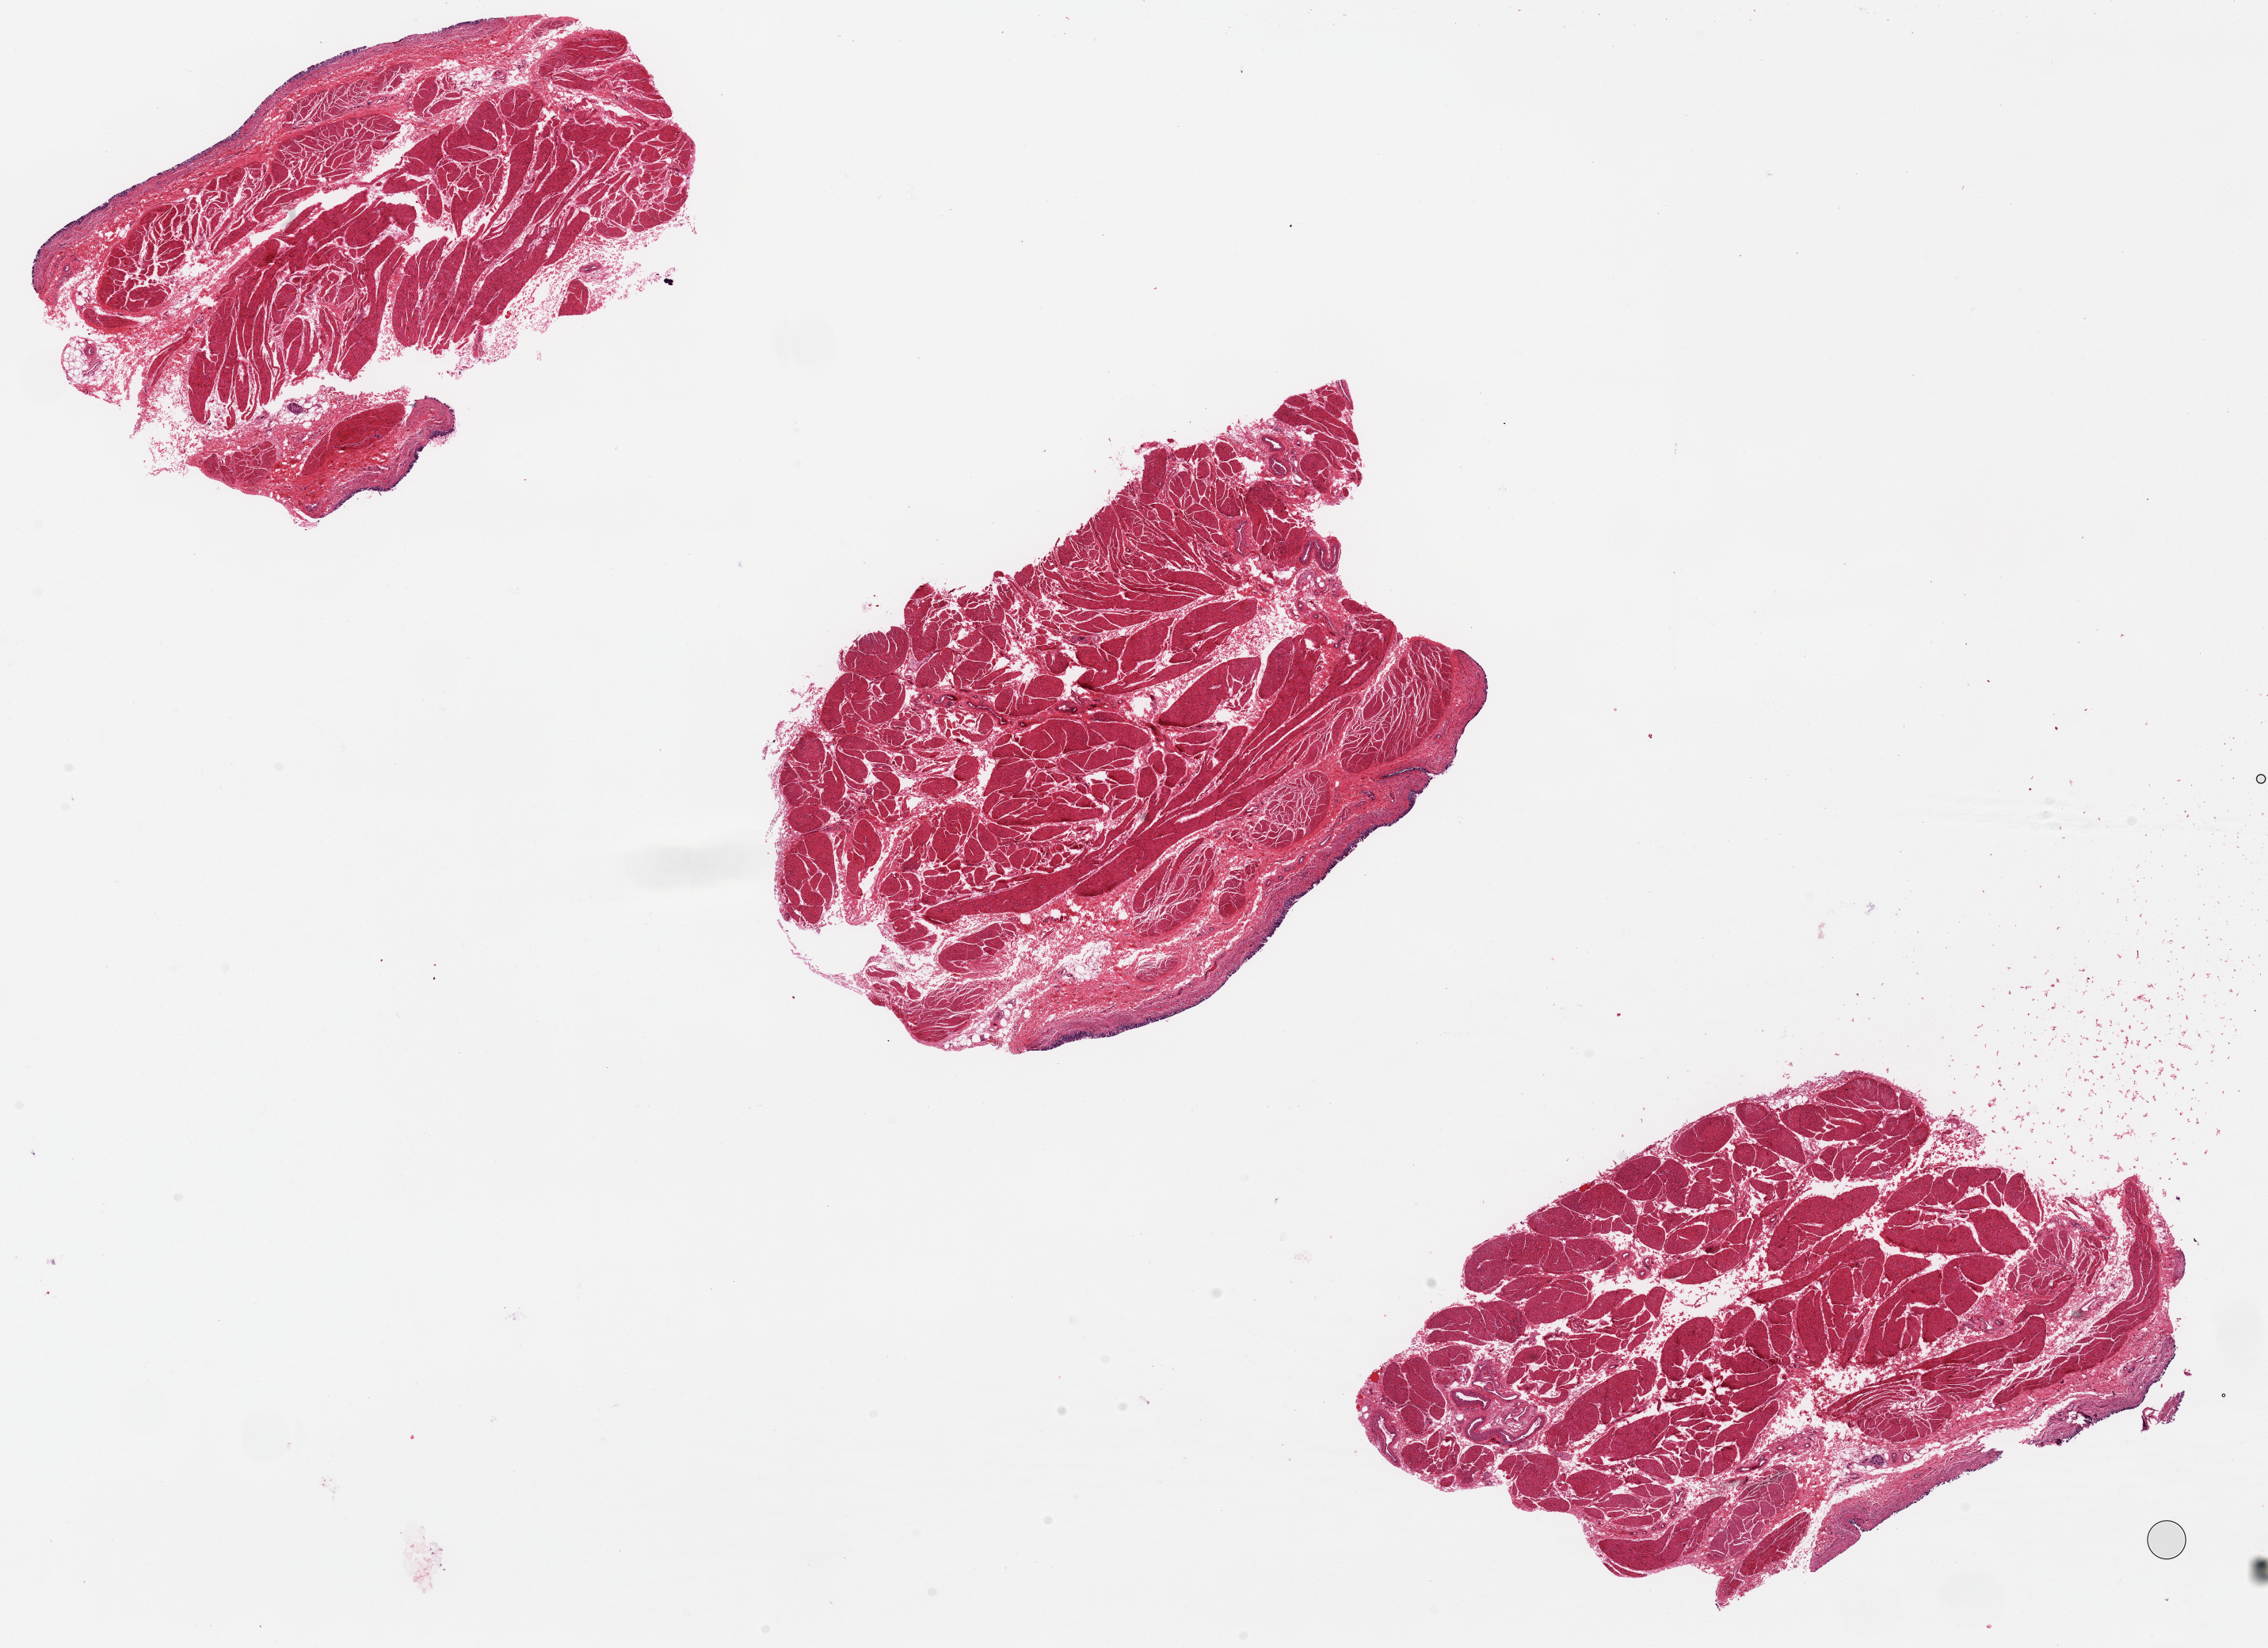
Hematoxylin and eosin (H&E) whole-slide image, brightfield — whole scanned area (about 22.6 x 16.4 mm, slide scanned at 20x) shown as a low-resolution overview; PAXgene-fixed, paraffin-embedded tissue; target tissue: urinary bladder; donor tissue sample. Donor: female.
Review note (as recorded): Mucosa largely sloughed.